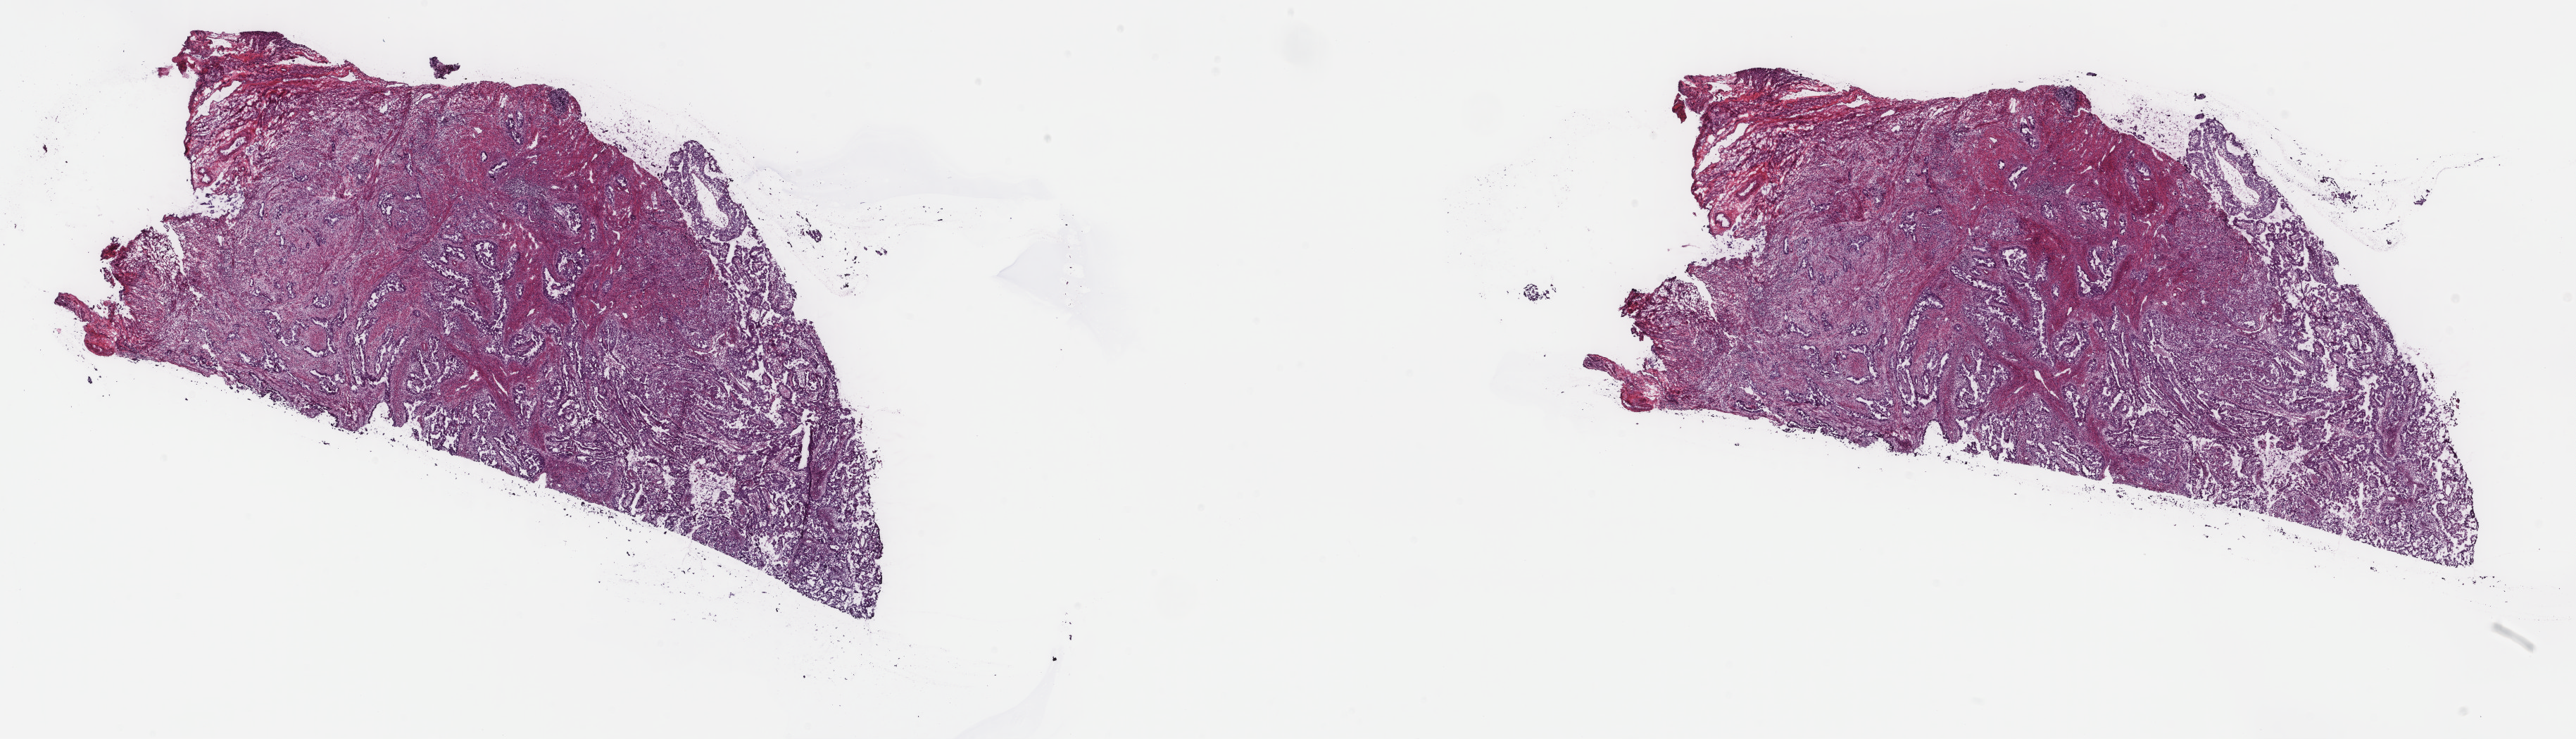
Whole-slide histology image, Hematoxylin and eosin (H&E) stained, a low-resolution overview of the entire scanned area, about 29.0 x 8.3 mm, frozen section, sample: primary tumour, uterus. Female patient; age at initial diagnosis 63 years. Histologic grade: G3 (poorly differentiated). Composition of this section per pathologist review: tumour cells 70%, tumour nuclei 70%, normal cells 0%, stromal cells 20%, necrosis 10%. Inflammatory infiltration, as recorded: lymphocyte infiltration 60%, monocyte infiltration 20%, neutrophil infiltration 10%.
* FIGO stage: IIIA
* histologic diagnosis: Serous cystadenocarcinoma, NOS
* lymph nodes positive (case pathology): 0 of 19 examined